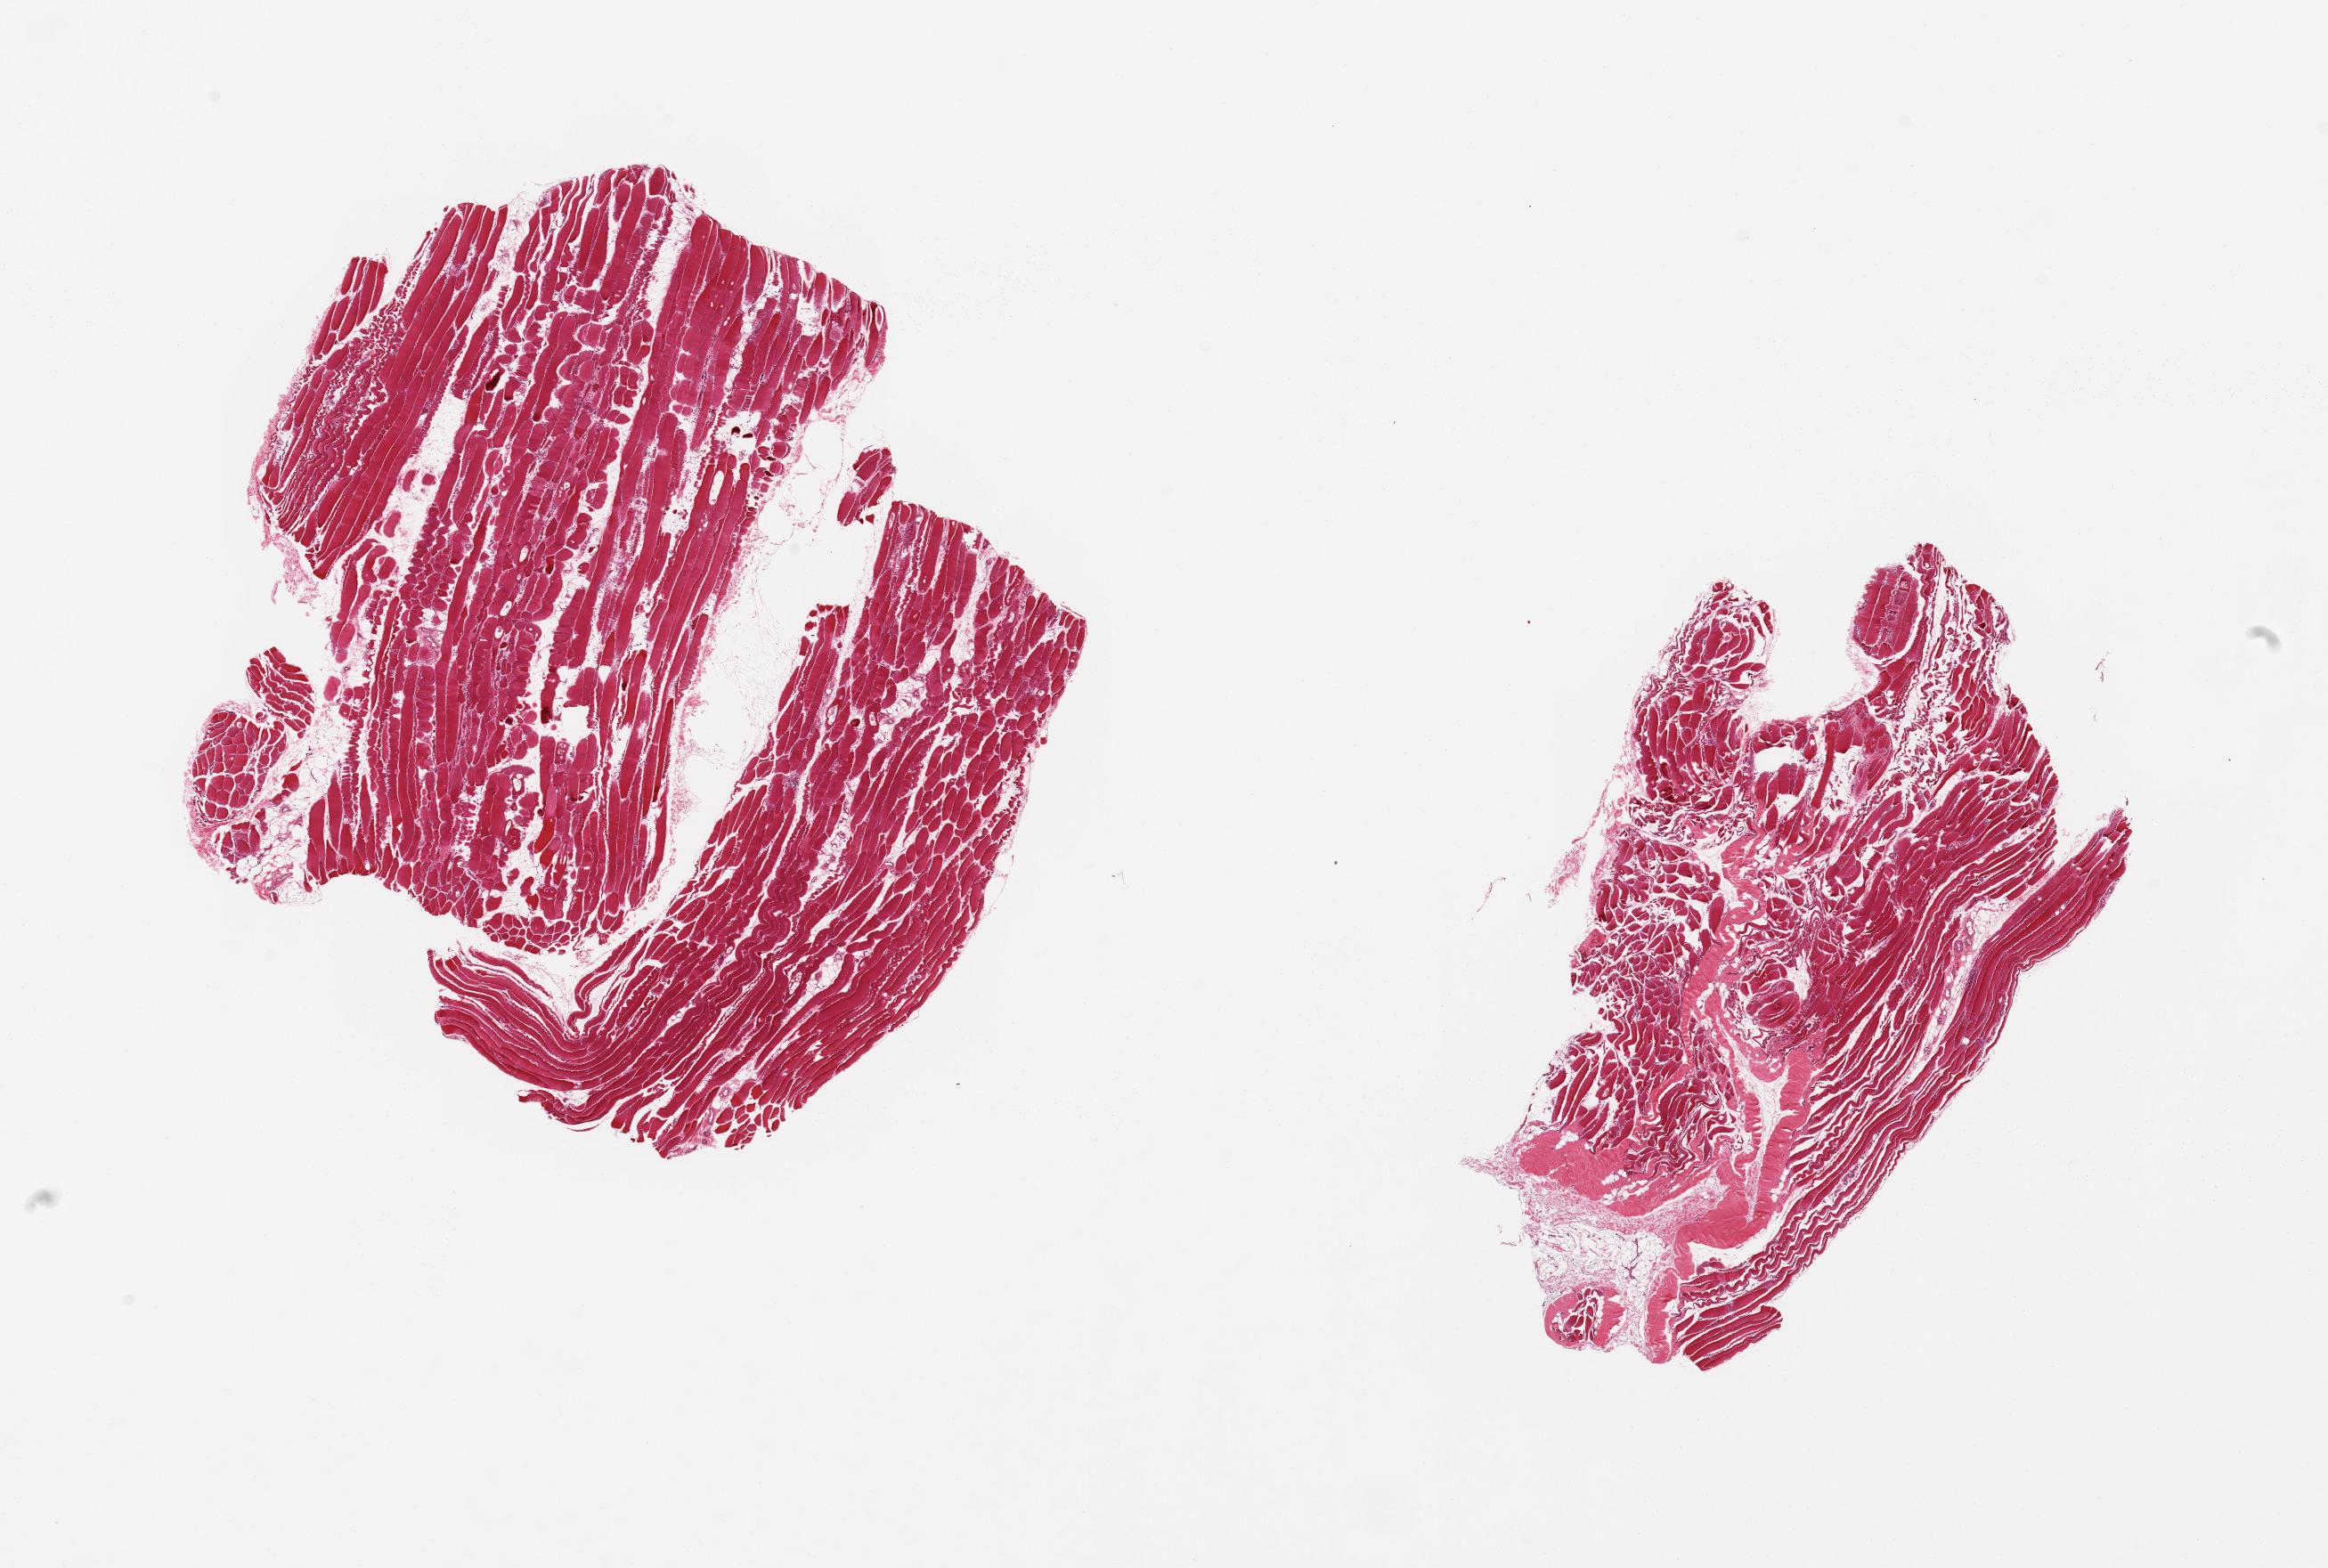
Digitized hematoxylin and eosin (H&E)-stained section, brightfield — whole scanned area (about 20.7 x 13.9 mm, acquisition: 20x scan) shown as a low-resolution overview; PAXgene-fixed paraffin-embedded (PFPE) section; target tissue: skeletal muscle; donor tissue sample. Donor sex: female.
Review note (as recorded): 2 pieces; focal atrophy.